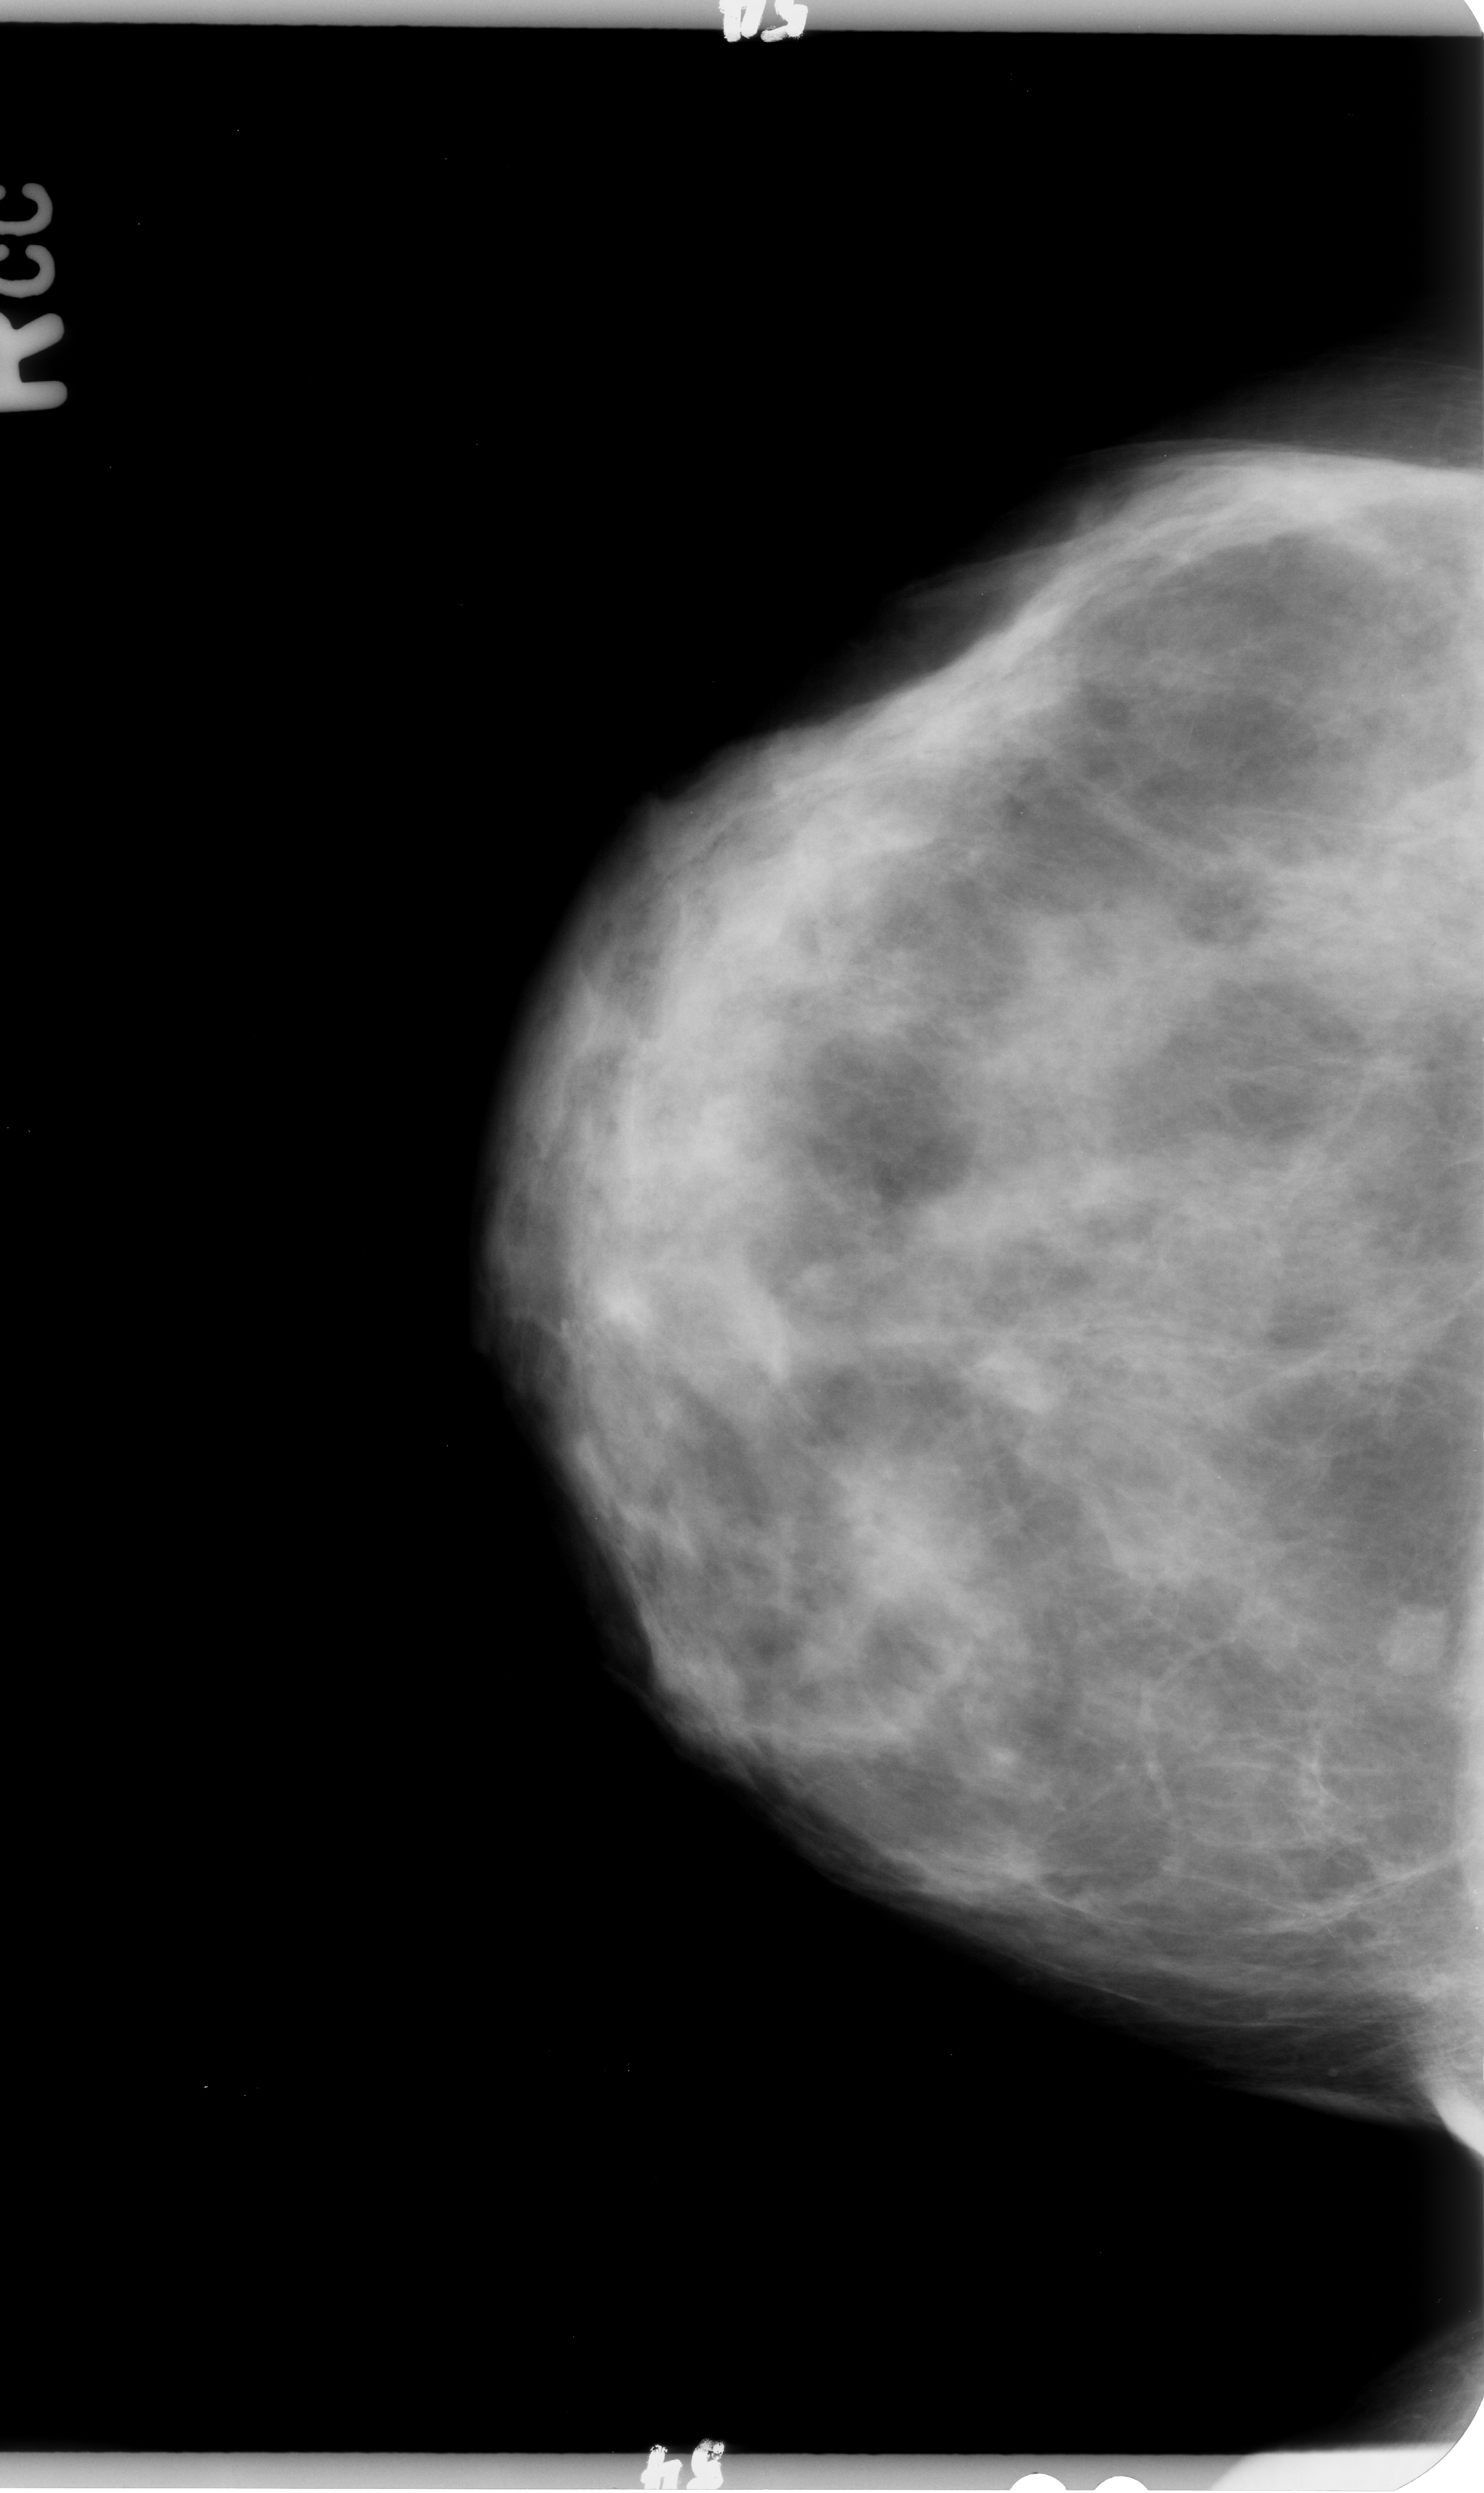
Digitized screen-film mammogram; right breast; craniocaudal (CC) view; BI-RADS breast density category 2 (scale 1–4); 1484 × 2493 image matrix.
Expert-marked regions of interest on this image (one box per marked abnormality):
- mass, shape lobulated, margins circumscribed; BI-RADS assessment category 4; pathology (as recorded): benign: box from (x=1375, y=1589) to (x=1466, y=1678) px